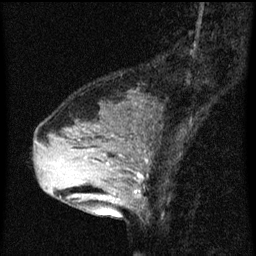
Breast MRI (dynamic contrast-enhanced), one sagittal slice; dynamic contrast-enhanced series, image 2 of 3 at this slice position (ordered by acquisition); 1.5 T; TE 4.2 ms, TR 8 ms; 256 × 256 image matrix, field of view 180 × 180 mm. Patient: female, 33 years.
Structures marked on this image (semi-automatically segmented with operator editing):
- analysis volume of interest (the breast-tissue region the enhancement analysis was run in; not a lesion): bounding box <61,126,150,213> (left, top, right, bottom; pixels)
- tumour enhancement mask (voxels above the 70 % enhancement threshold inside the analysis volume of interest): <93,160,143,195>